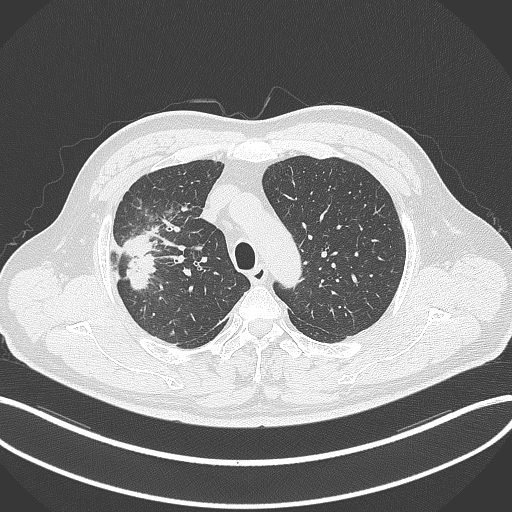
Chest CT, one axial slice; 120 kVp; lung window (W 1500 / L -600 HU); 1 mm slice thickness; 512 × 512 image matrix. Male patient, age 55 years. From the clinical record (not read from this slice): clinical TNM (as recorded): T3 N2 M1.
Structures marked on this image (rectangle marked by the reading radiologist):
- lung tumour (recorded histology: adenocarcinoma): bounding box <117,229,161,289> (left, top, right, bottom; pixels)